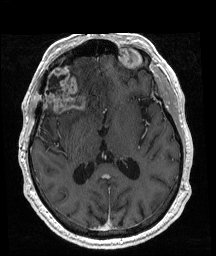
Brain MRI from a brain-tumour surgery series, one axial slice; slice 97 of 192 in the series (ordered by position); T1-weighted post-contrast; 1 mm slice thickness; 216 × 256 image matrix, field of view 211 × 250 mm. From the clinical record (not read from this slice): histopathology: Glioblastoma; WHO grade: 4; IDH mutation: no; tumour location: Right Frontal.
Annotated regions visible in this slice (expert manual segmentation):
- previous resection cavity: bounding box <48,76,64,95> (left, top, right, bottom; pixels)